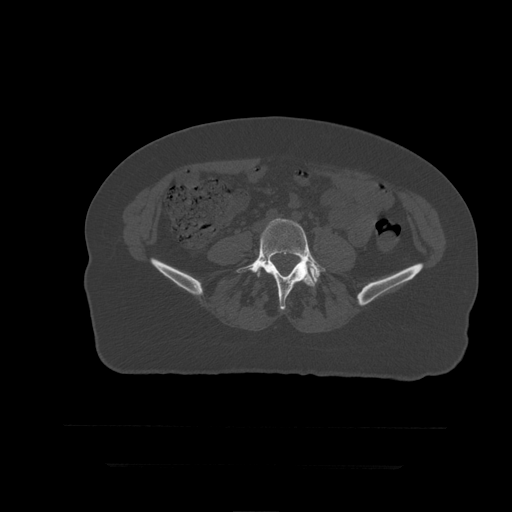
CT including the spine, one axial slice; slice 75 of 399 in the series (ordered by position); reconstruction kernel STANDARD; 120 kVp; bone window (W 1800 / L 400 HU); 1.25 mm slice thickness; 512 × 512 image matrix. Patient age 41 years. Case-level facts recorded for this patient, not image findings: primary cancer: breast.
Structures marked on this image (semi-automatically segmented with operator editing):
- L5 vertebra: bounding box <237,219,326,310> (left, top, right, bottom; pixels)